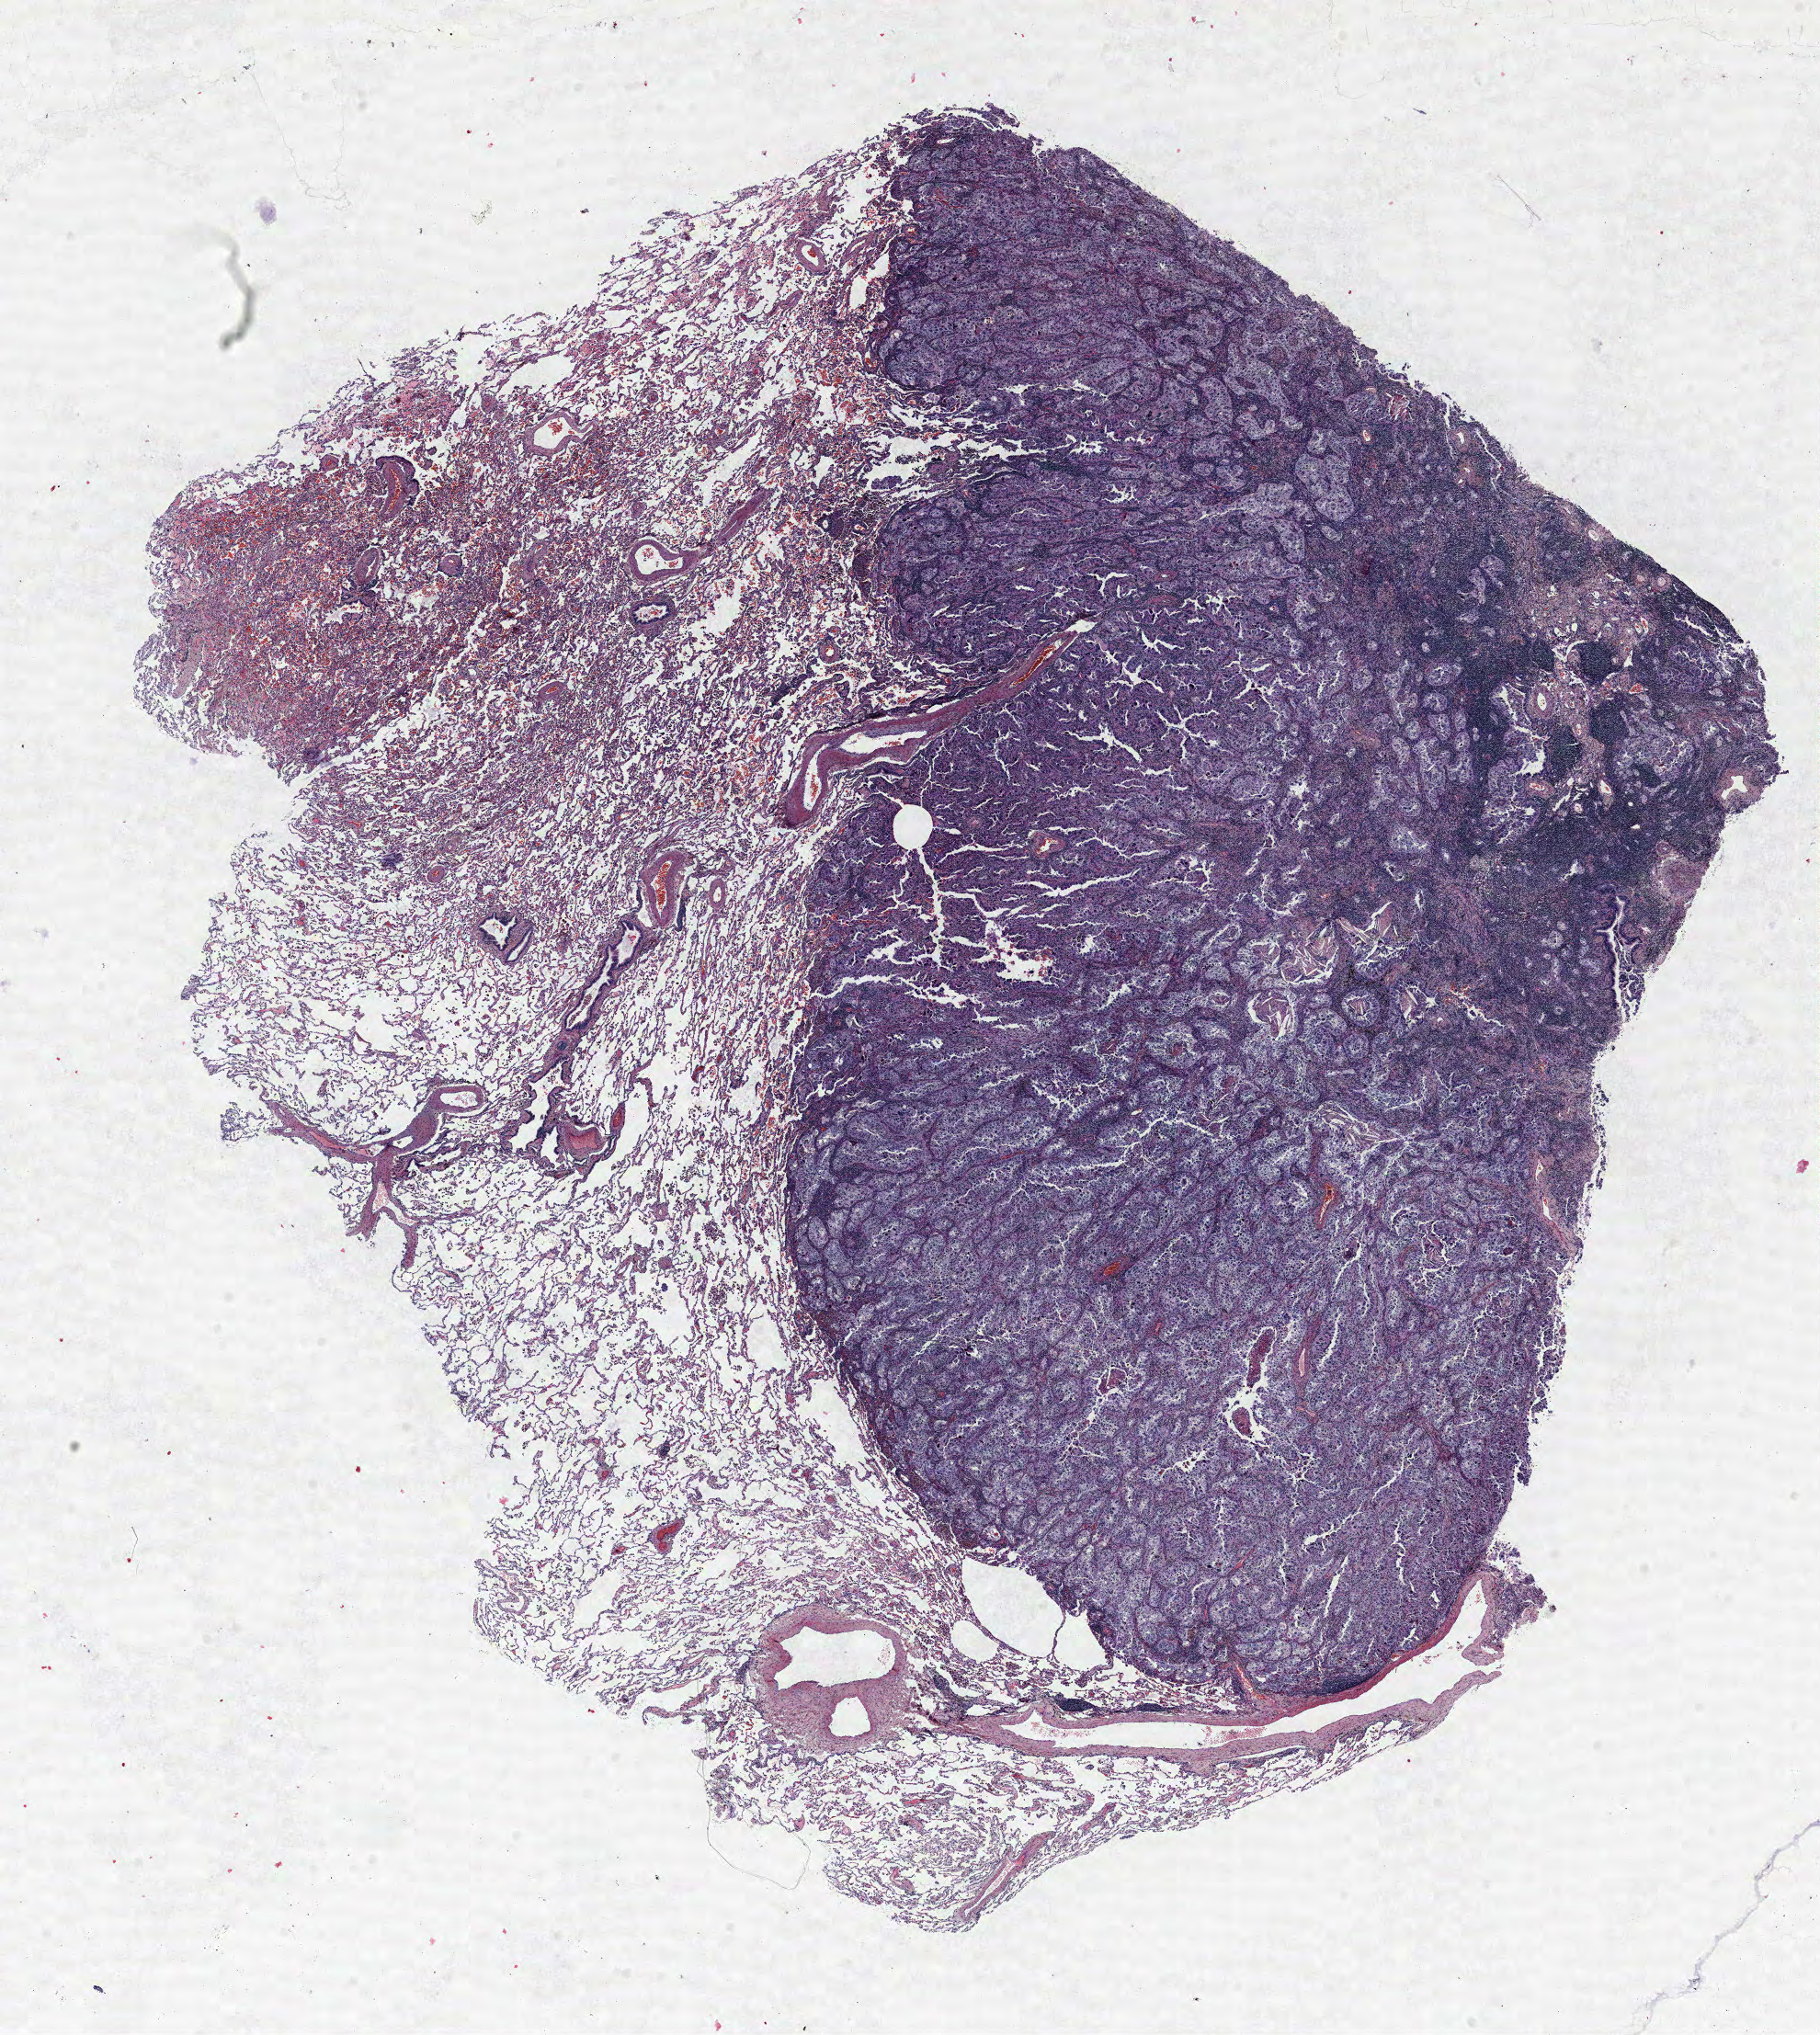
H&E-stained whole-slide image — shown as a low-resolution overview of the whole scanned area (about 15.8 x 17.7 mm); FFPE section; lung tissue. Male patient, aged 57 at enrolment. Current smoker at enrolment. Grade: poorly differentiated (G3).
Participant's lung-cancer diagnosis: Adenocarcinoma, NOS. Primary tumour location (clinical record): right lower lobe. Tumour size (pathology): 24 mm. ICD-O-3 topography: lower lobe of lung (C34.3). Stage (AJCC 6th edition): IA.